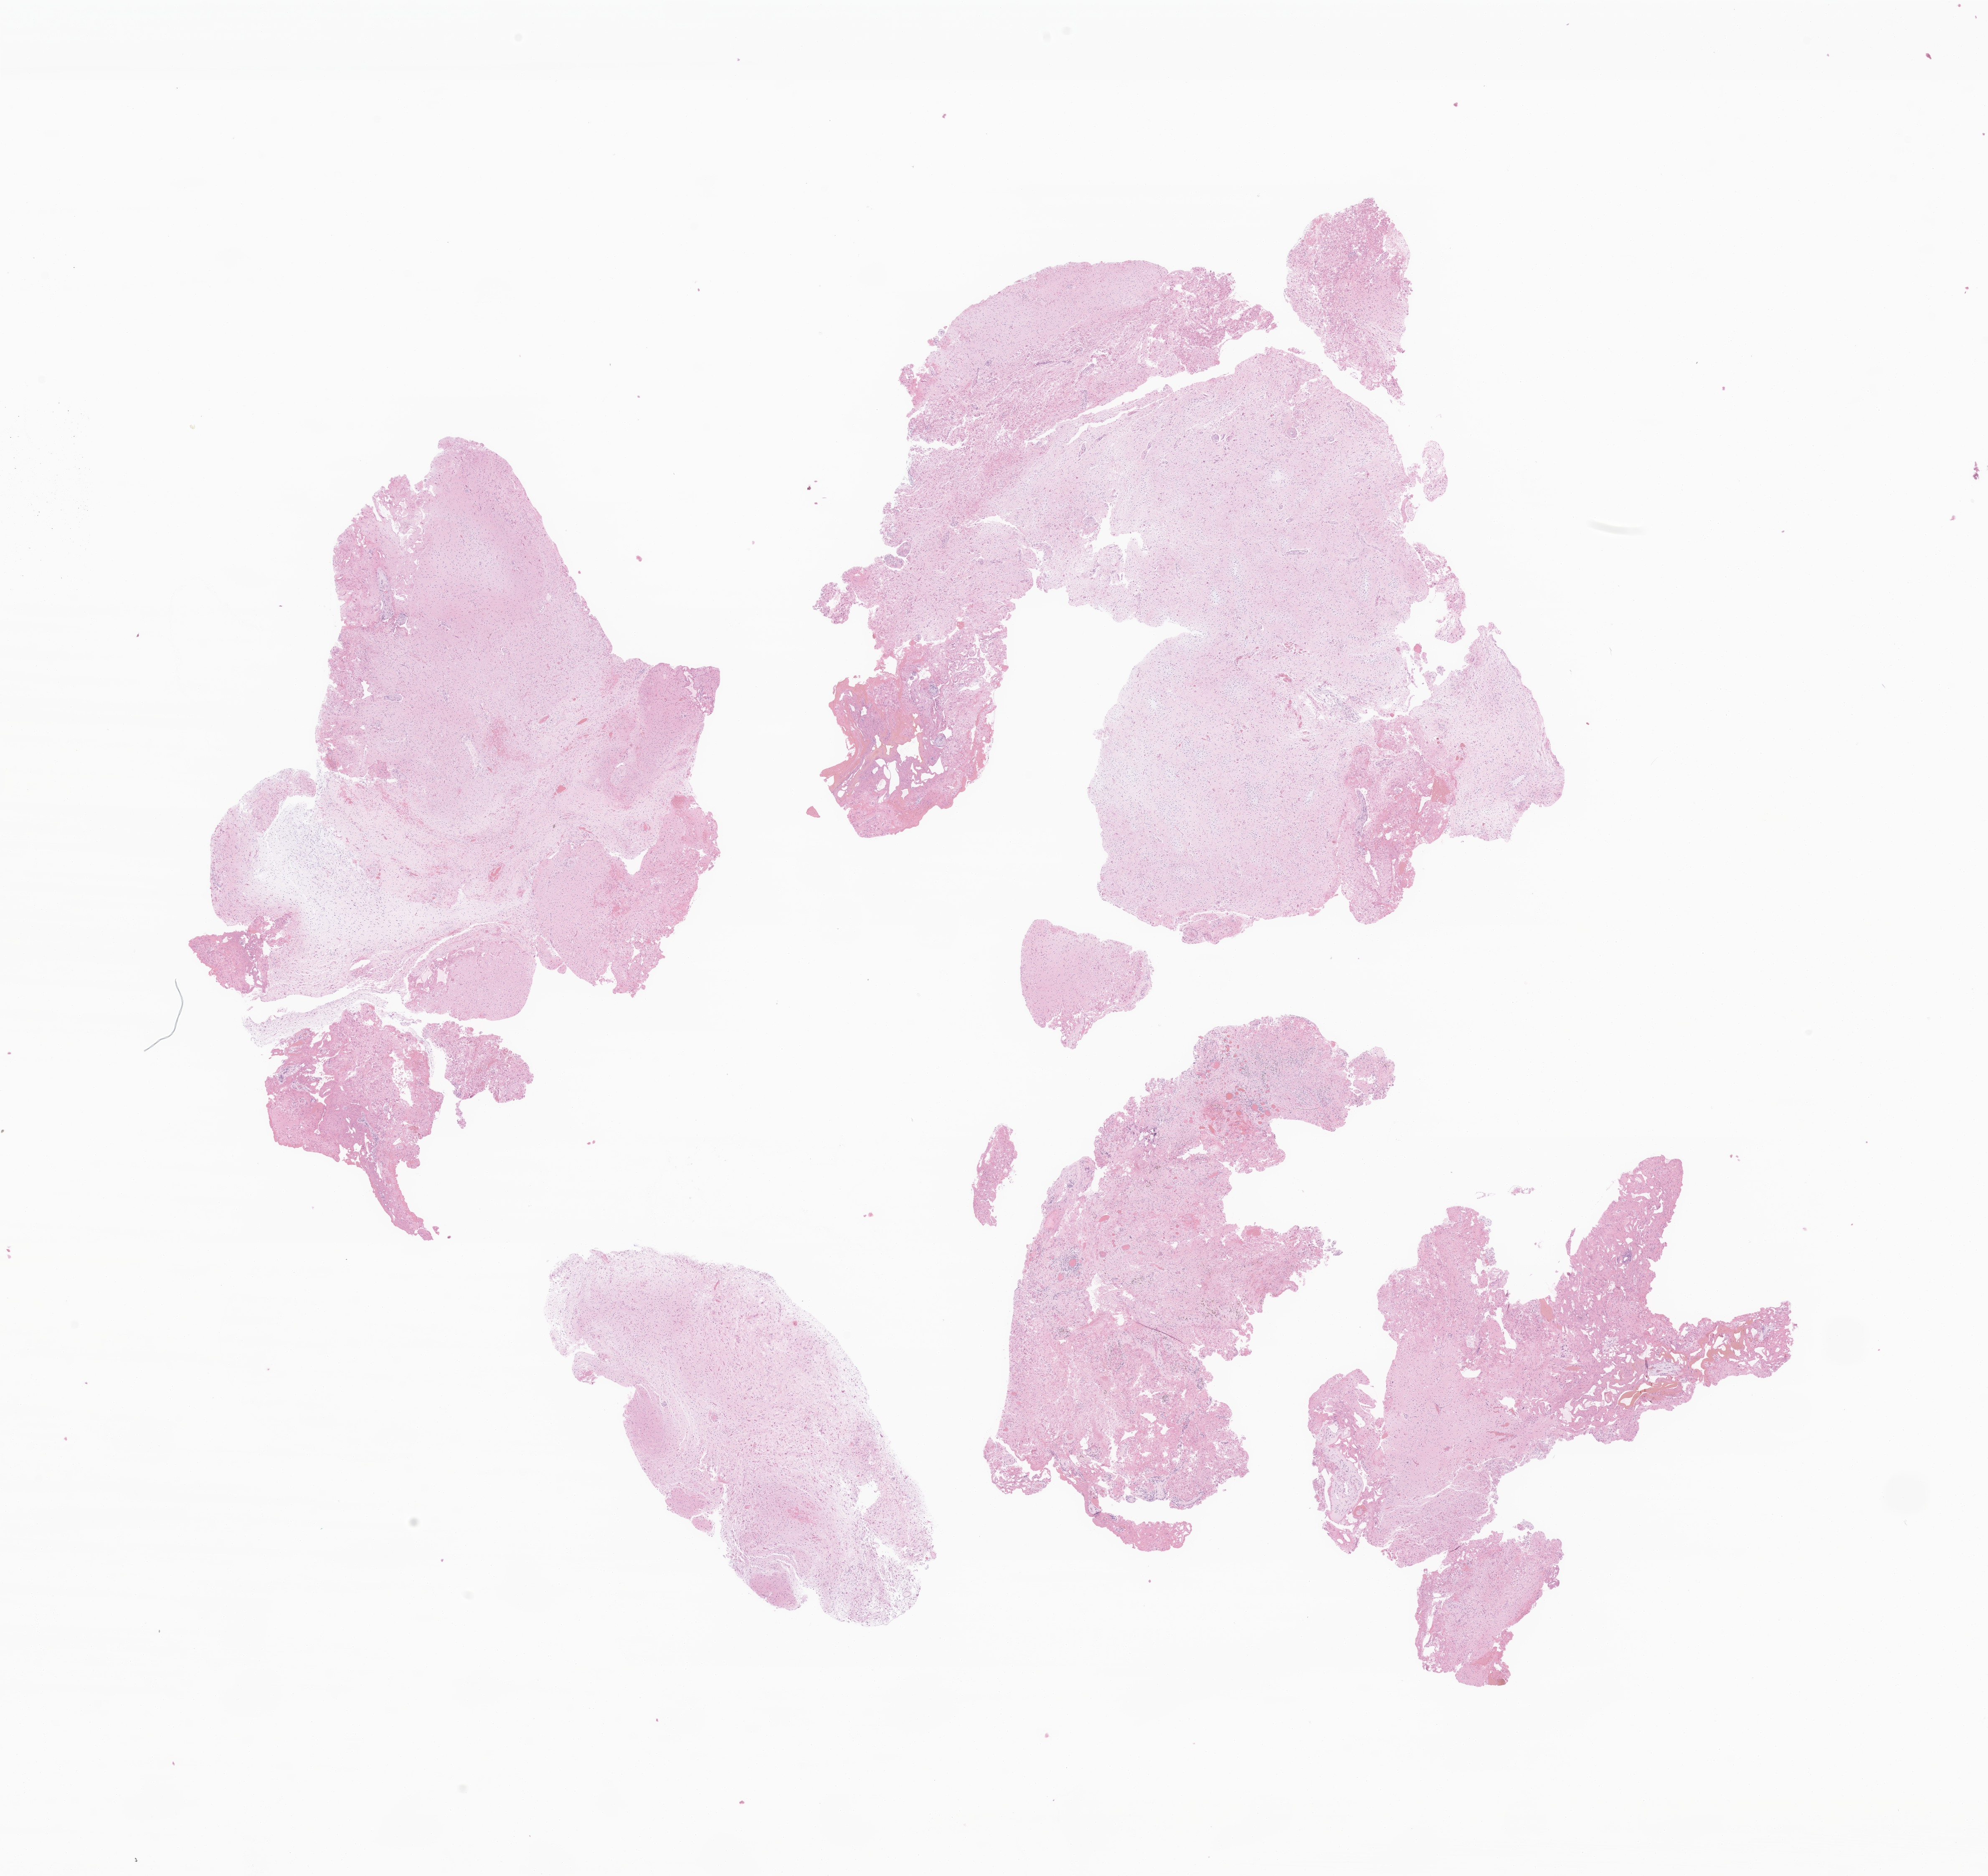
Whole-slide image, haematoxylin and eosin stain of tumor tissue from the cerebrum — a low-resolution overview of the entire scanned area, about 20.1 x 18.9 mm; formalin-fixed paraffin-embedded section. Female patient, age 174 months (14 years 6 months).
Recorded diagnosis: Pilocytic astrocytoma.